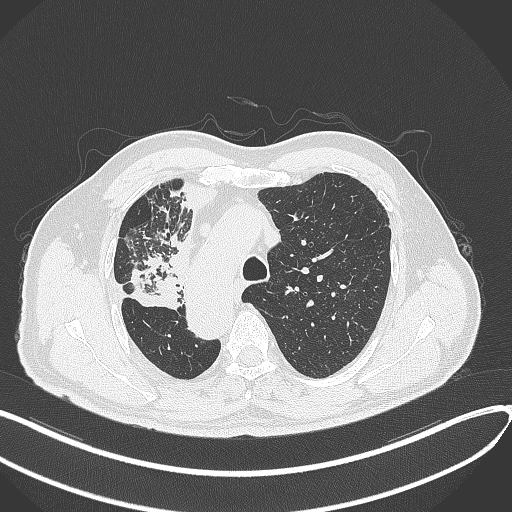
Chest CT, one axial slice. Position 235 of 300 along the scan axis. 120 kVp. Lung window (W 1500 / L -600 HU). 1 mm slice thickness. 512 × 512 image matrix, field of view 400 × 400 mm. Patient: male, 67 years. From the clinical record (not read from this slice): clinical TNM (as recorded): T2a N0 M0.
Annotated regions visible in this slice (rectangle marked by the reading radiologist):
- lung tumour (recorded histology: squamous cell carcinoma): box from (x=127, y=250) to (x=184, y=311) px